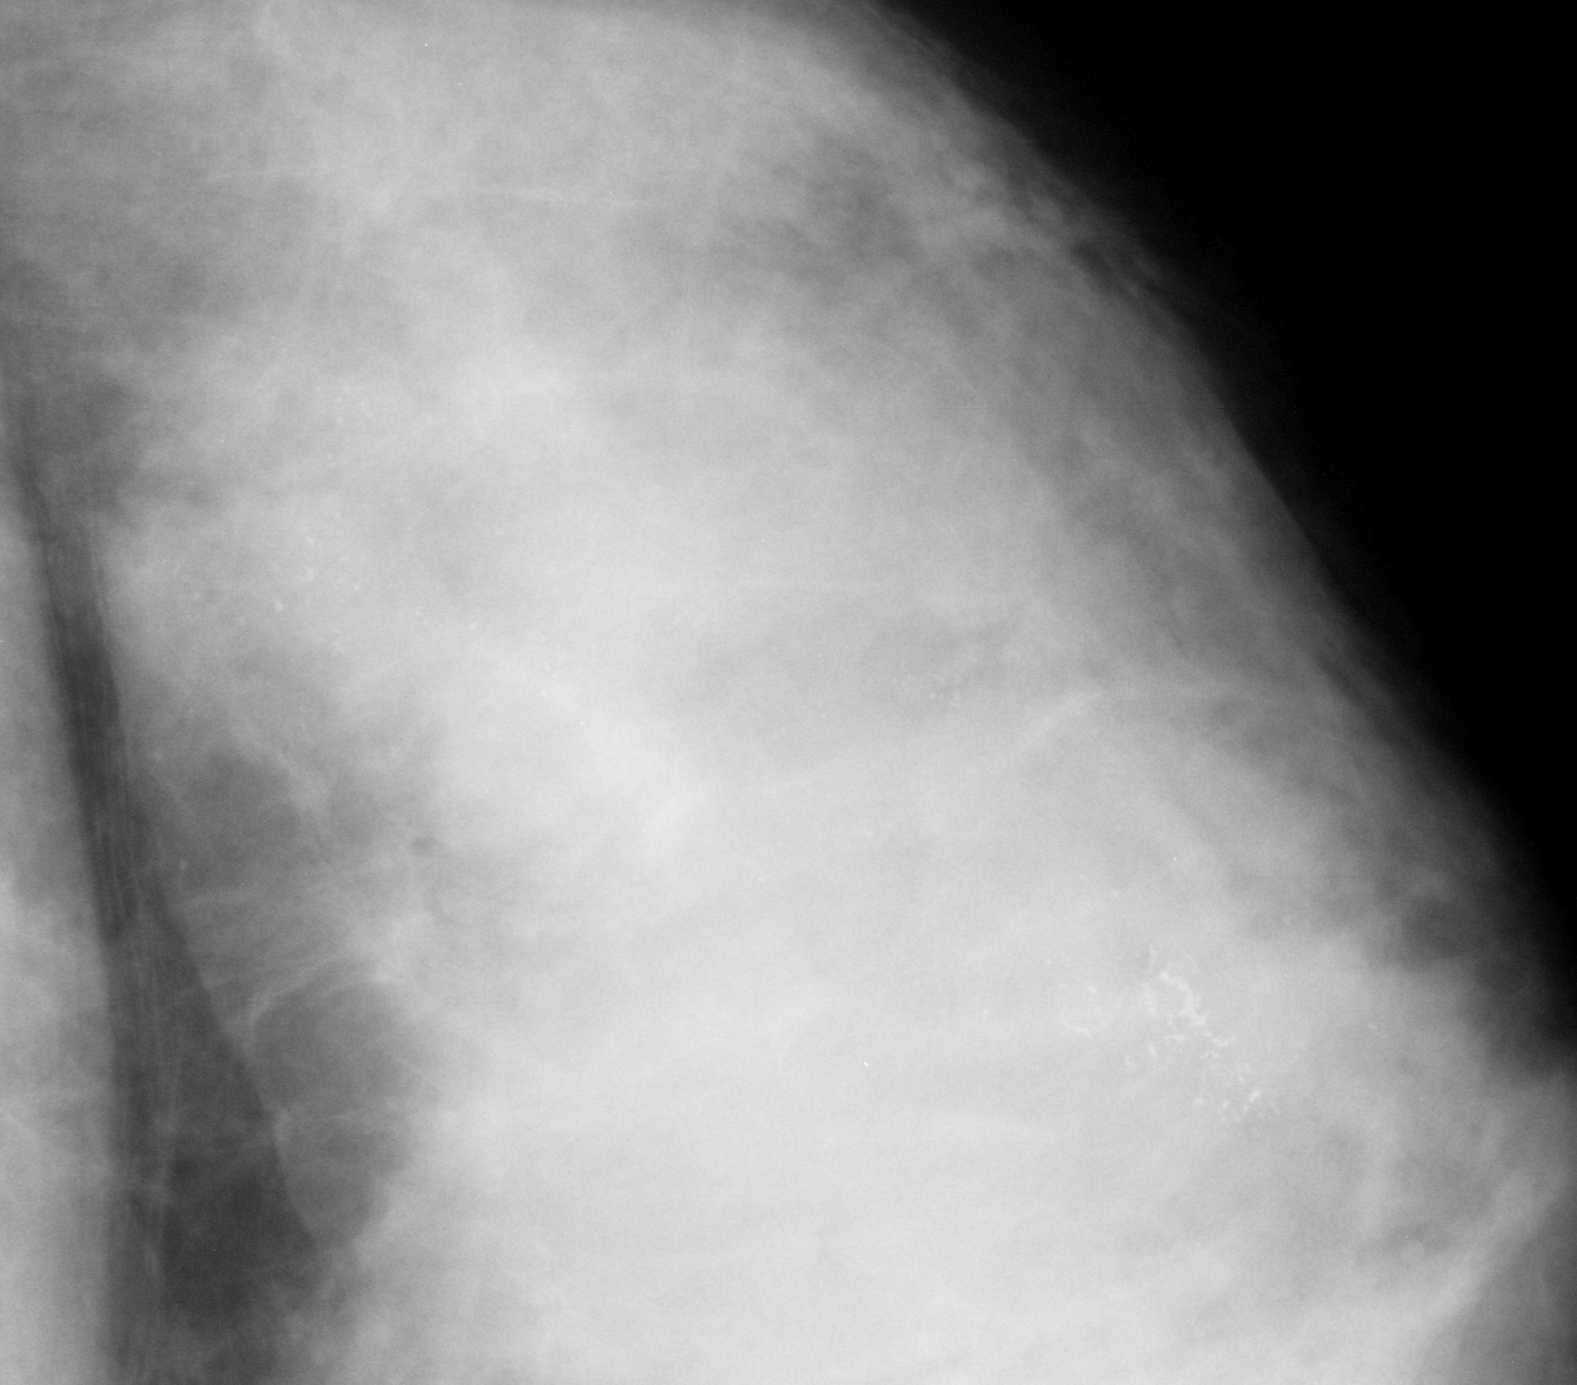
Crop from a digitized film mammogram around one marked abnormality; left breast; CC view; BI-RADS breast density category 4 (scale 1–4).
- Calcifications, morphology amorphous / pleomorphic, distribution segmental; BI-RADS assessment category 5; pathology (as recorded): malignant.